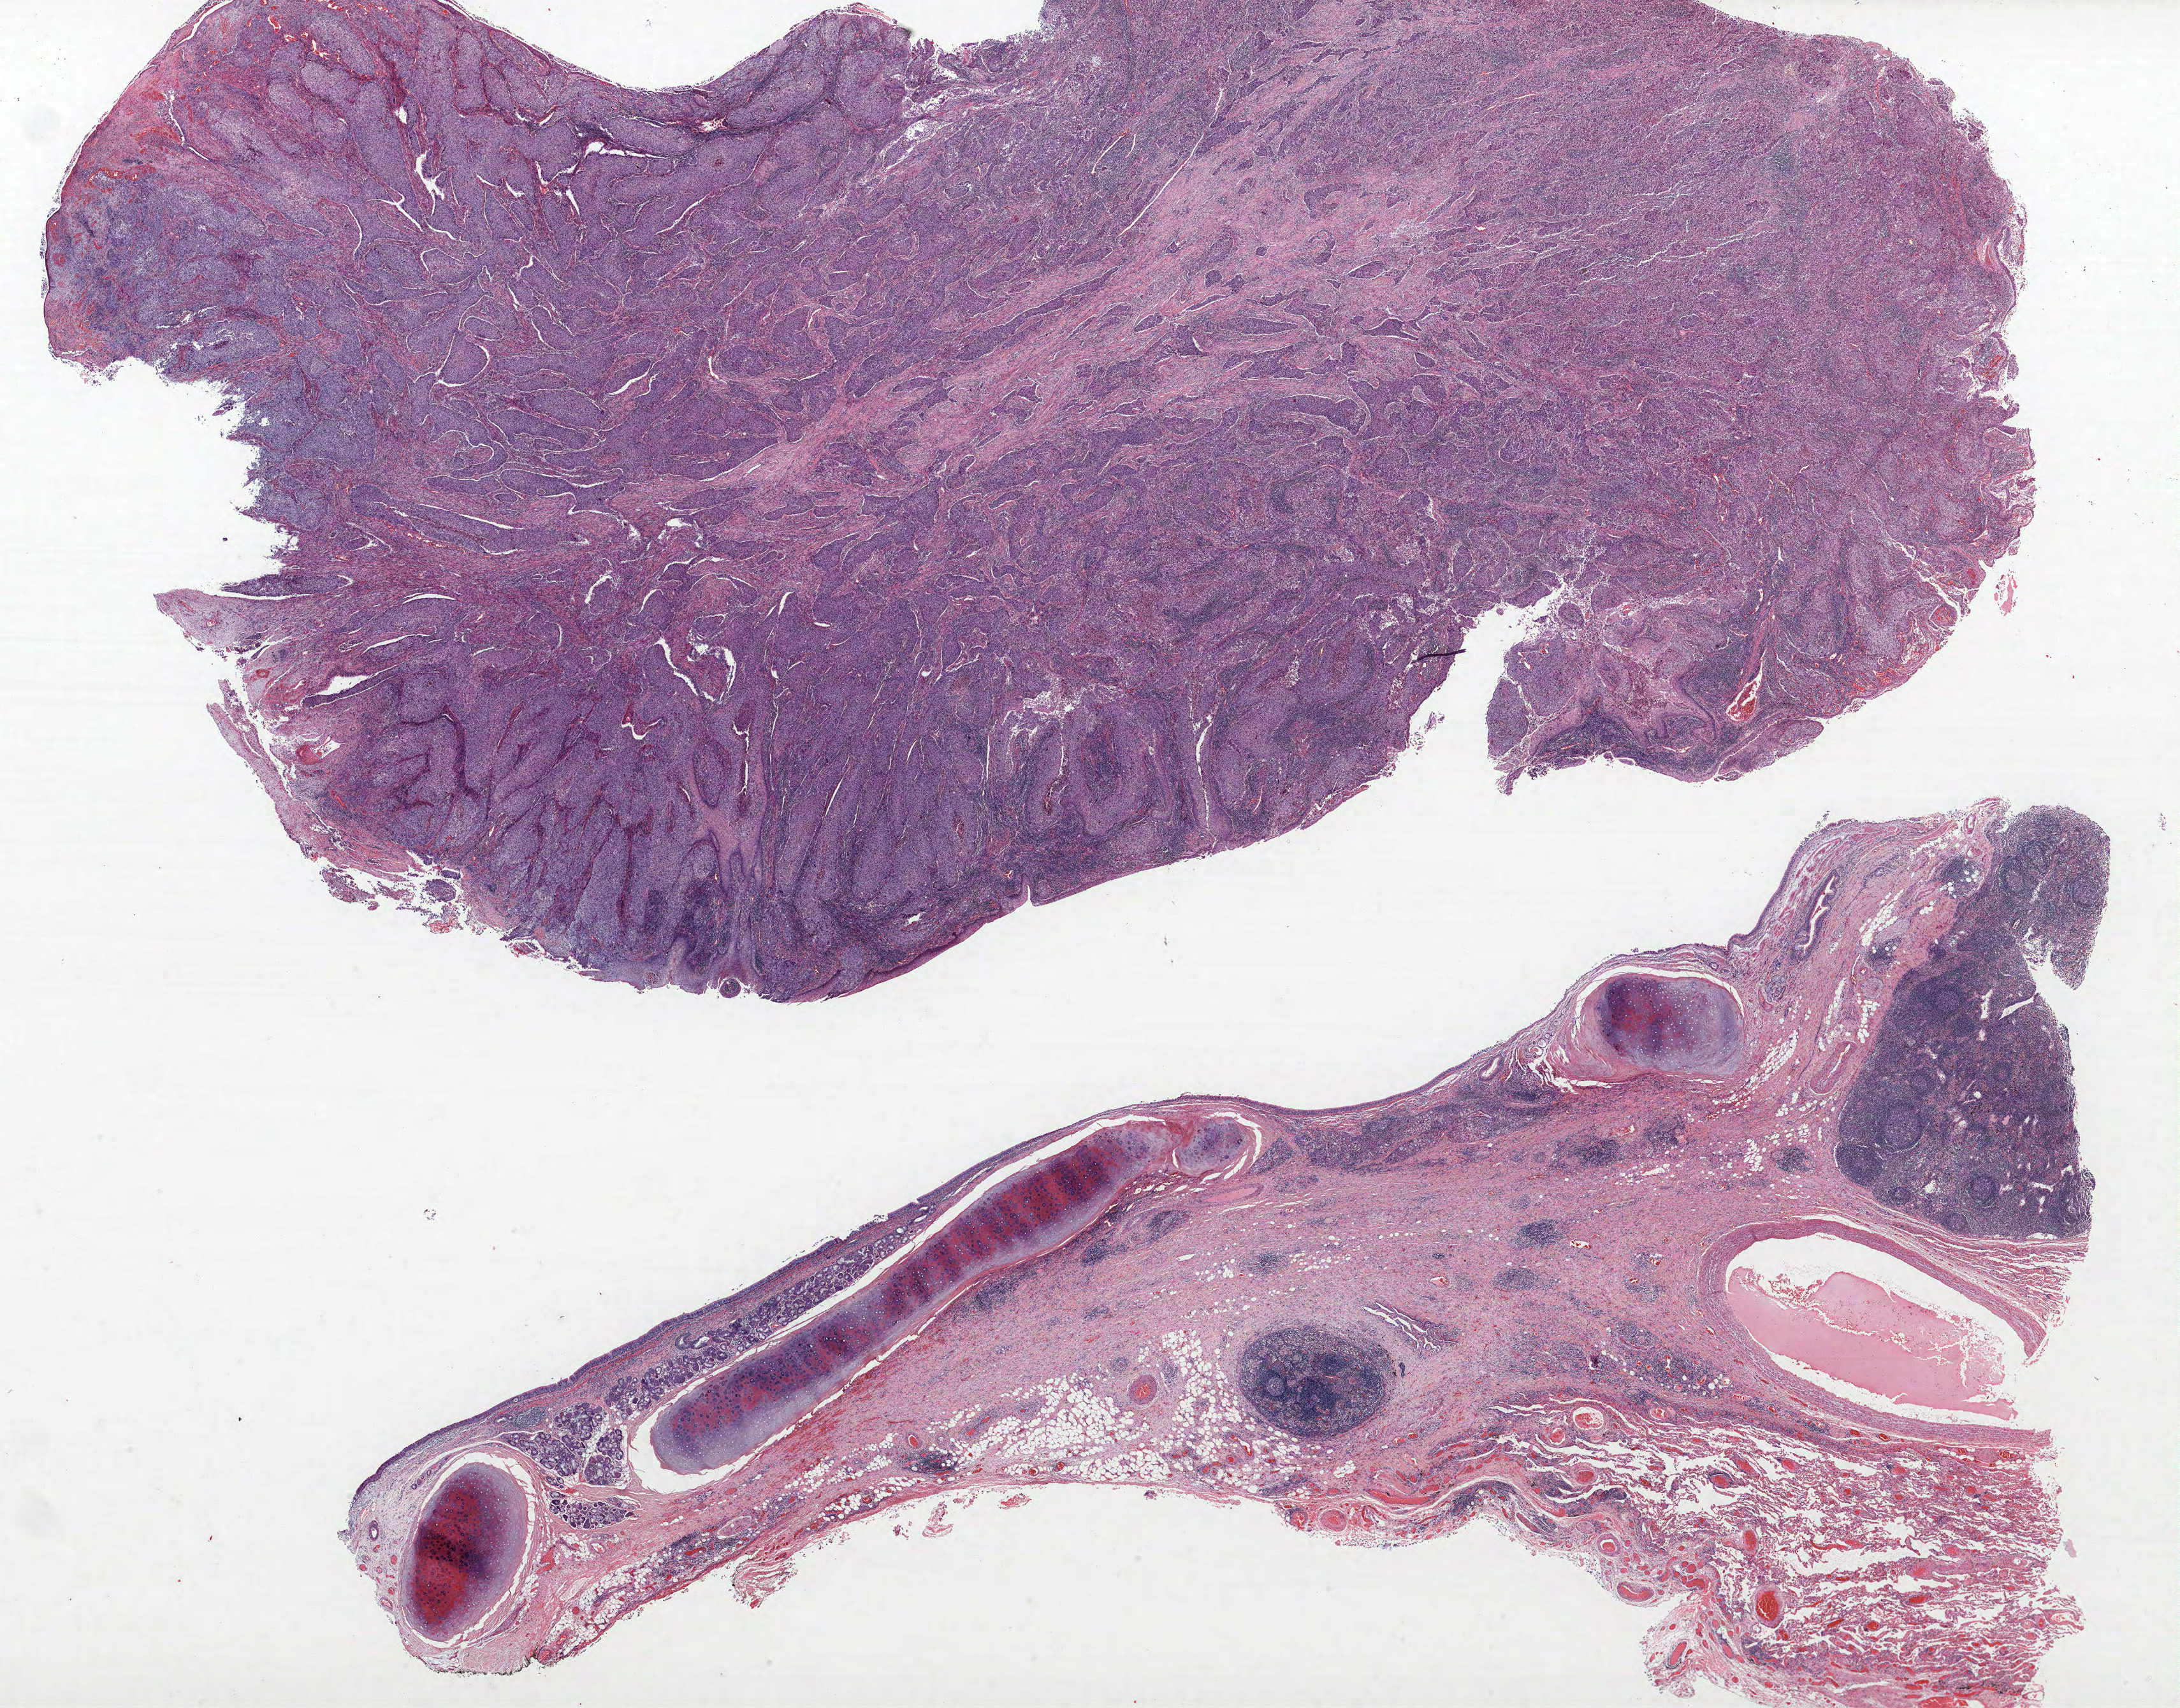
Whole-slide histology image, Hematoxylin and eosin (H&E) stained — a low-resolution overview of the entire scanned area, about 27.4 x 21.4 mm (acquisition: 40x scan). FFPE section. Lung. Male patient, aged 66 at enrolment. Grade: moderately differentiated (G2).
* tumour size (pathology): 39 mm
* participant's lung-cancer diagnosis: Squamous cell carcinoma, NOS
* stage (AJCC 6th edition): IIB
* ICD-O-3 topography: upper lobe of lung (C34.1)
* primary tumour location (clinical record): right upper lobe